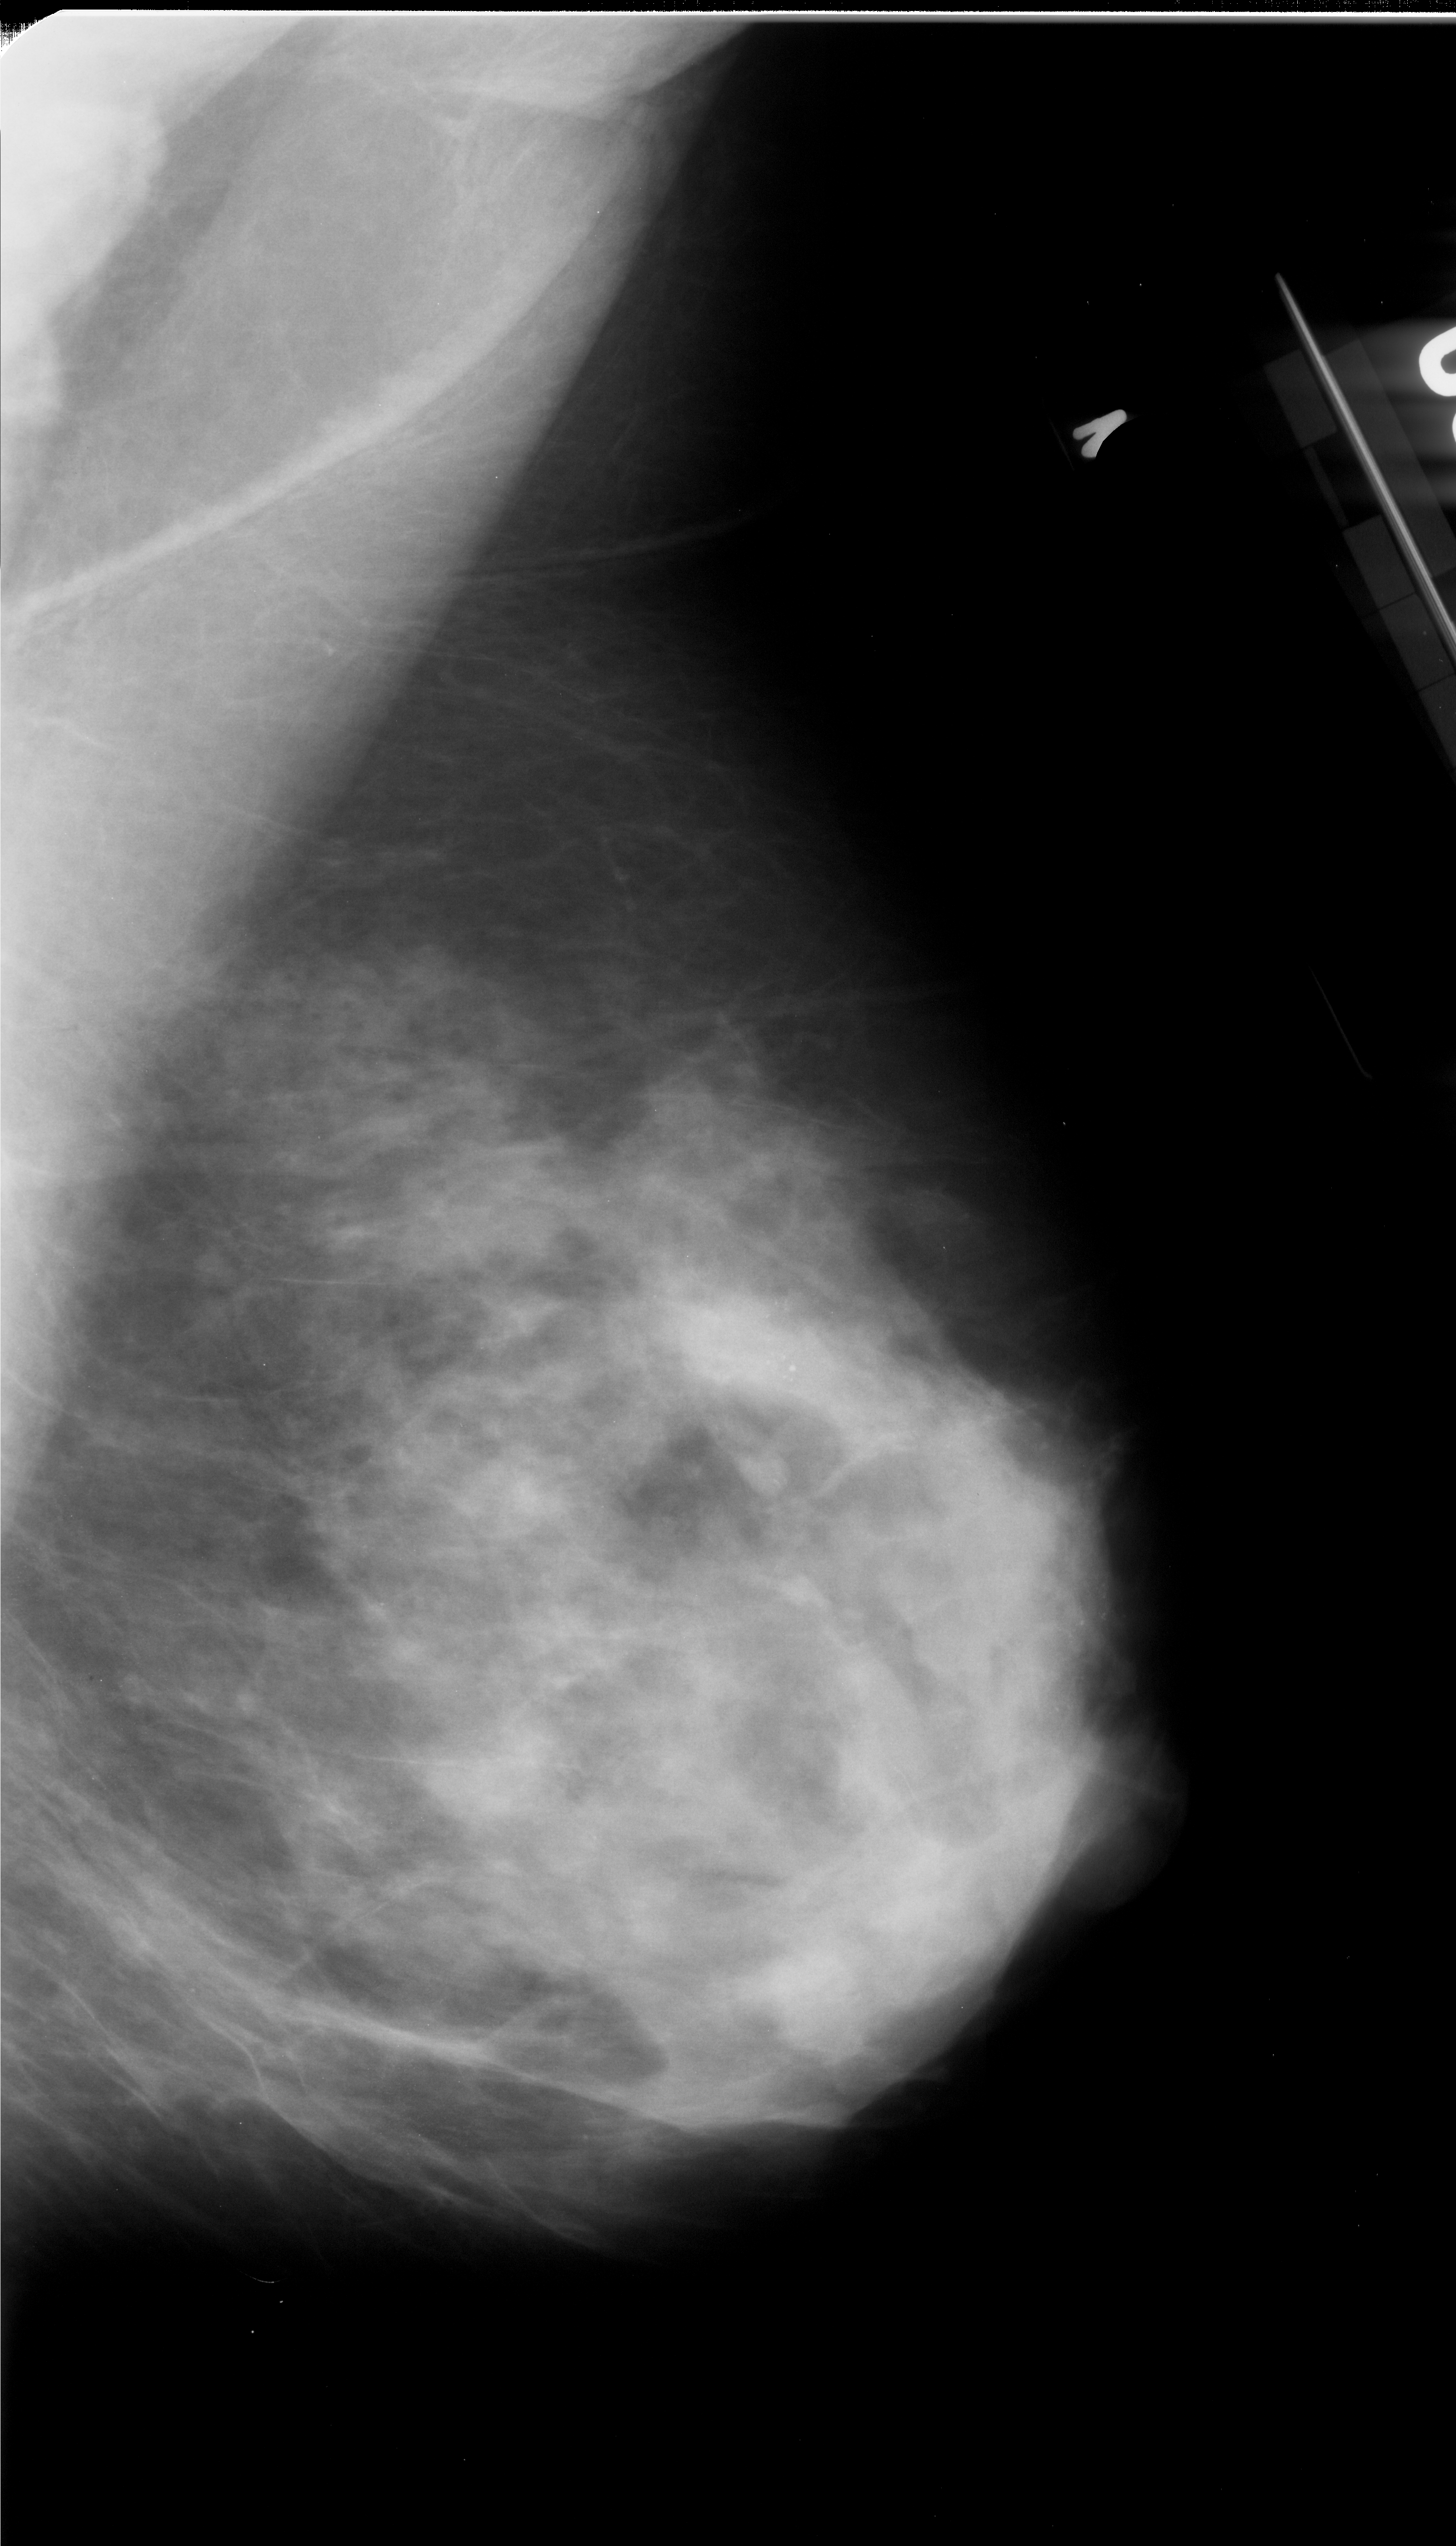
Scanned film-screen mammogram, right breast, MLO view, breast composition: extremely dense (BI-RADS density category 4 of 4).
Marked abnormality: calcifications, morphology pleomorphic, distribution clustered; BI-RADS assessment category 4; pathology (as recorded): malignant.